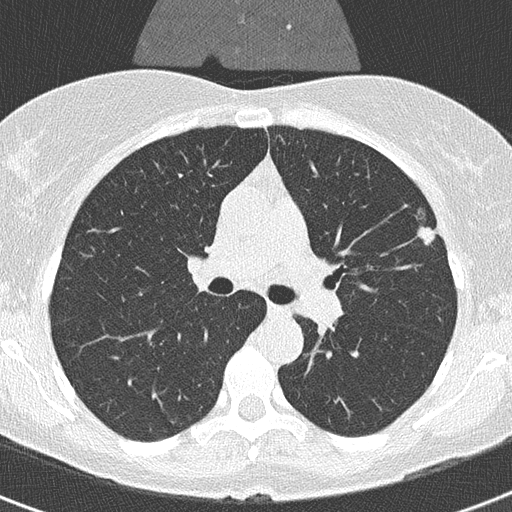
Axial slice from a low-dose chest CT screening exam; second annual screen; lung window (W 1500 / L -600 HU); 2 mm slice thickness; 120 kVp; 512 × 512 image matrix, field of view 290 × 290 mm. Female participant, aged 56 years at enrolment. Former smoker at enrolment.
Lesion marked by an expert reader, bounding box <404,201,454,255> (left, top, right, bottom; pixels). Screening reader's record for this exam (one nodule recorded; not confirmed to be the boxed lesion): non-calcified nodule or mass ≥4 mm, left upper lobe, 20 × 9 mm, smooth margins, soft tissue attenuation, pre-existing on the prior screen: yes; interval growth: yes. Official screen result: positive, other.